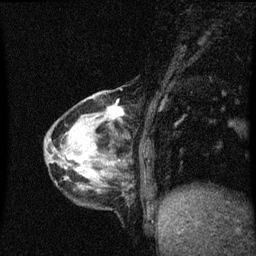
Breast MRI (dynamic contrast-enhanced), one sagittal slice. Slice 15 of 60 in the series (ordered by position). Dynamic contrast-enhanced series, image 2 of 3 at this slice position (ordered by acquisition). 1.5 T. TE 4.2 ms, TR 8.4 ms. 2 mm slice thickness. 256 × 256 image matrix. Female patient, age 64 years. From the clinical record (not read from this slice): setting: breast cancer imaged before/during neoadjuvant chemotherapy; receptor status: HR-positive, HER2-negative.
Annotated regions visible in this slice (semi-automatic segmentation, software-assisted and operator-edited):
- analysis volume of interest (the breast-tissue region the enhancement analysis was run in; not a lesion): bounding box [x1, y1, x2, y2] px = [65, 96, 130, 157]
- tumour enhancement mask (voxels above the 70 % enhancement threshold inside the analysis volume of interest): [111, 106, 124, 117]